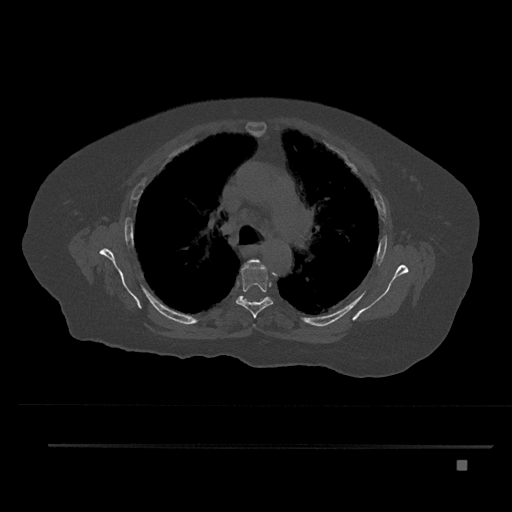
CT including the spine, one axial slice. Position 567 of 797 along the scan axis. Reconstruction kernel Br40s/3. Bone window (W 1800 / L 400 HU). 0.5 mm slice thickness. 512 × 512 image matrix, field of view 437 × 437 mm. Female patient, age 76 years. Case-level facts recorded for this patient, not image findings: primary cancer: lung.
Outlined on this slice (semi-automatically segmented with operator editing):
- T4 vertebra: bounding box <249,259,260,327> (left, top, right, bottom; pixels)
- T5 vertebra: <236,262,274,318>
- T6 vertebra: <259,298,265,303>